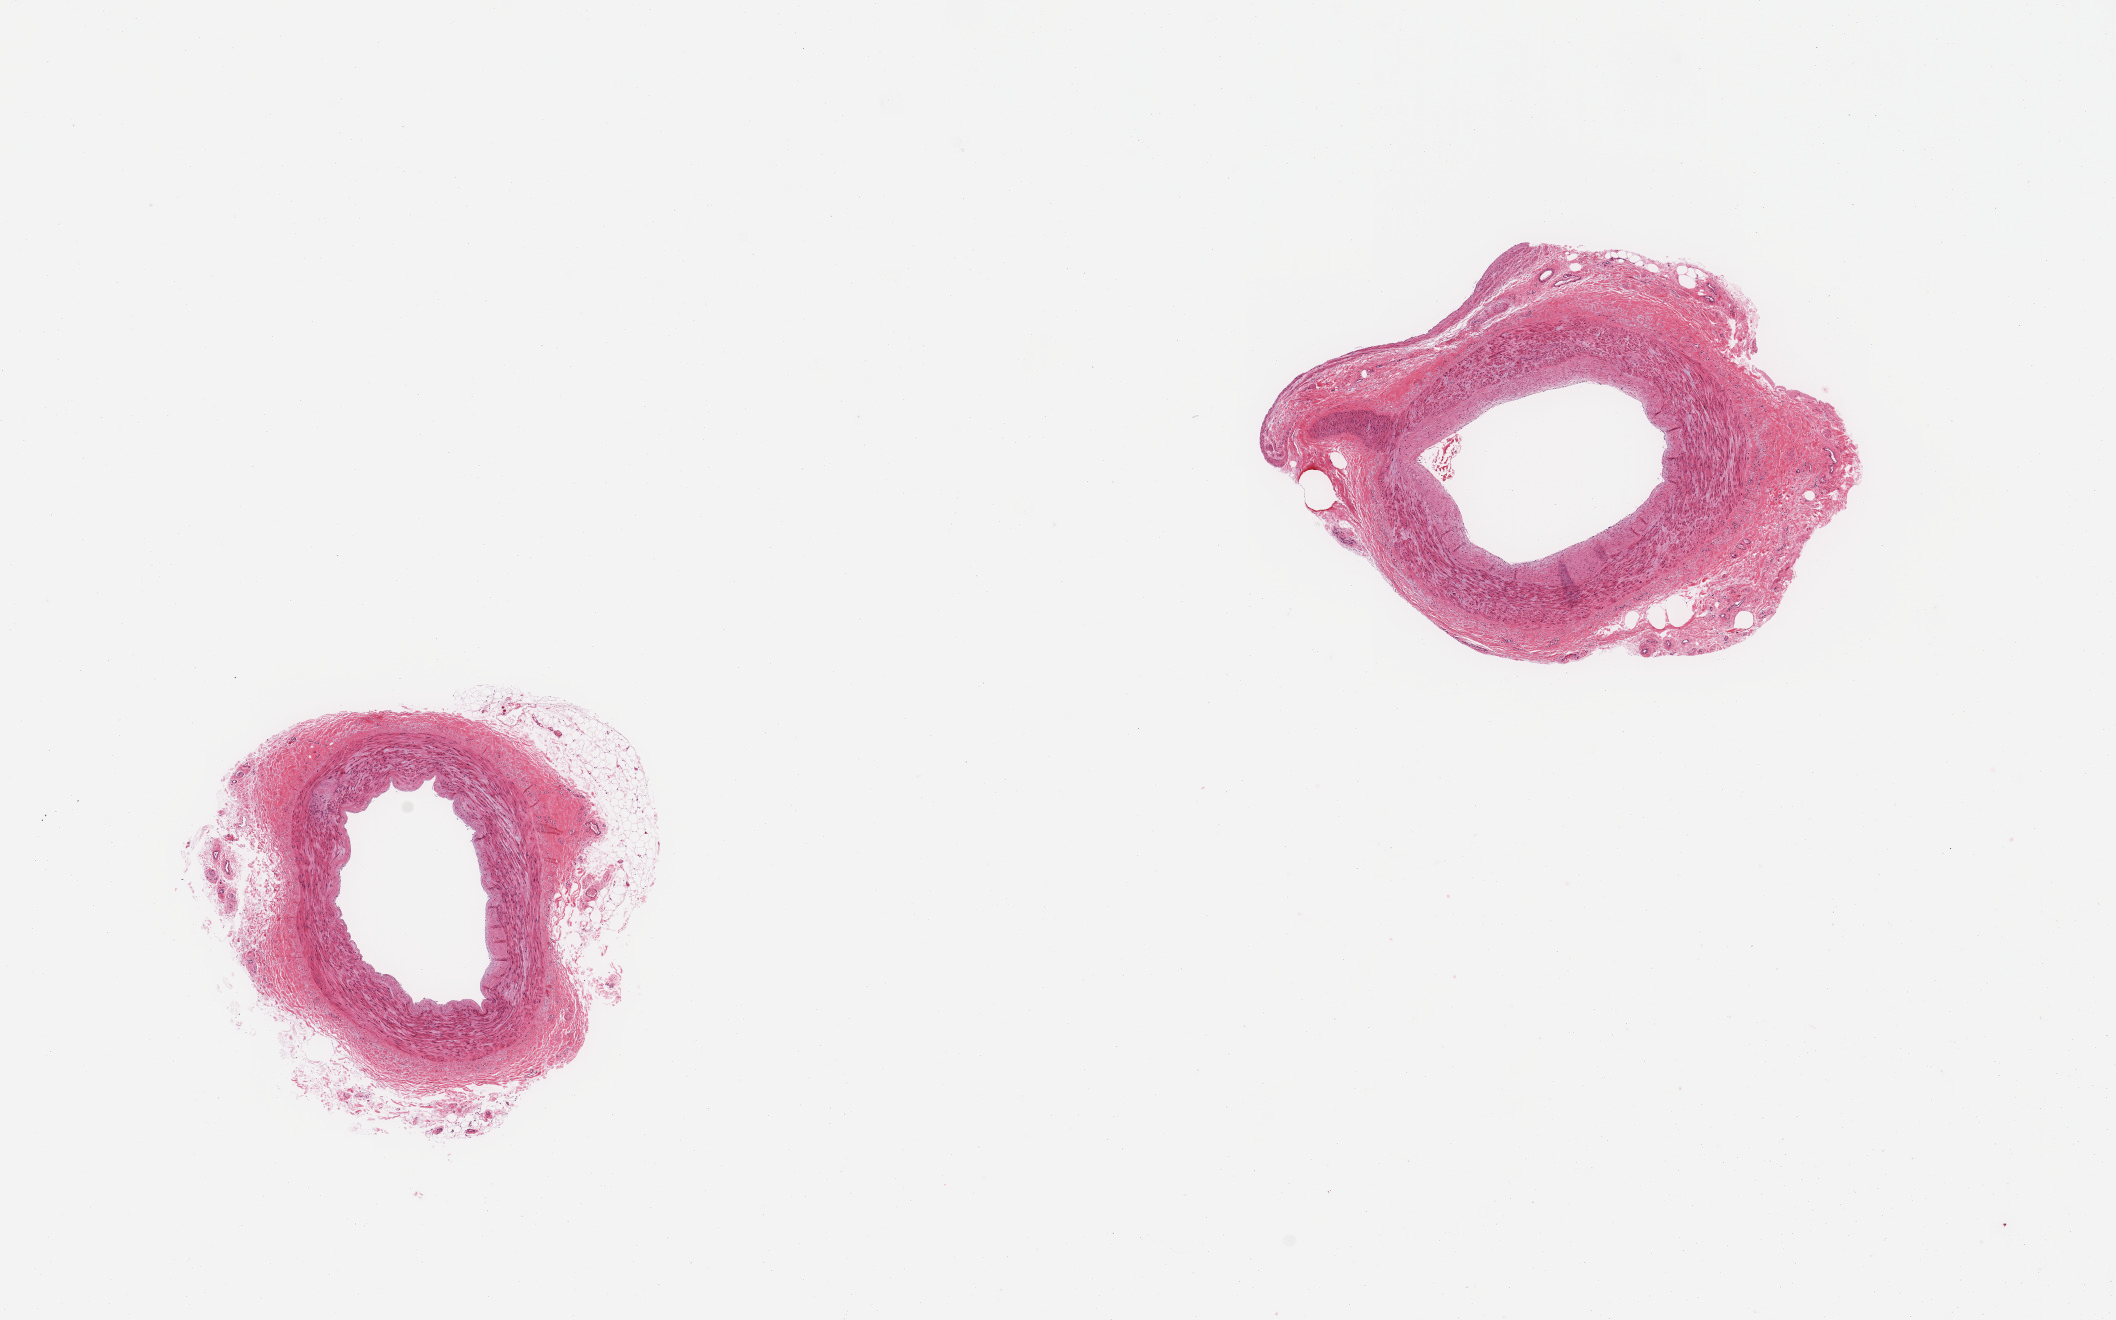
Whole-slide image, H&E stain — a low-resolution overview of the entire scanned area, about 16.7 x 10.4 mm (acquisition: 20x scan). PAXgene-fixed, paraffin-embedded tissue. Sampled site (target tissue): tibial artery. Tissue donor sample. Donor: male.
Review note (as recorded): 2 pieces; mild flat intimal fibrous plaques; up to 0.5 mm fibrofatty cuff.